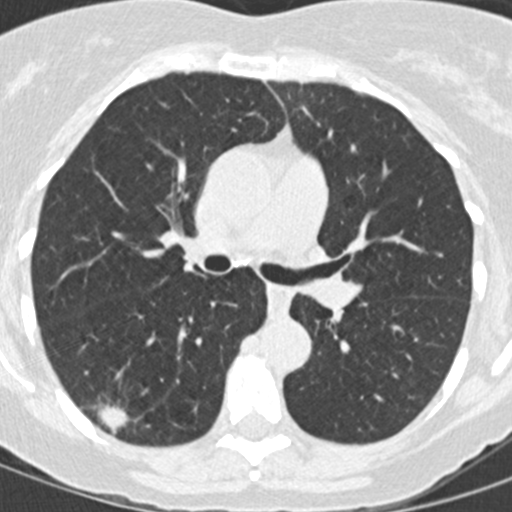
Low-dose screening chest CT, one axial slice; slice 86 of 146 in the series (ordered by position); 120 kVp; lung window (W 1500 / L -600 HU); 2 mm slice thickness; 512 × 512 image matrix, field of view 270 × 270 mm.
Structures marked on this image (outlined manually by an expert reader):
- lesion 1 (tumor, lower lobe of right lung): bounding box (x1, y1, x2, y2) in pixels: (97, 404, 129, 435)